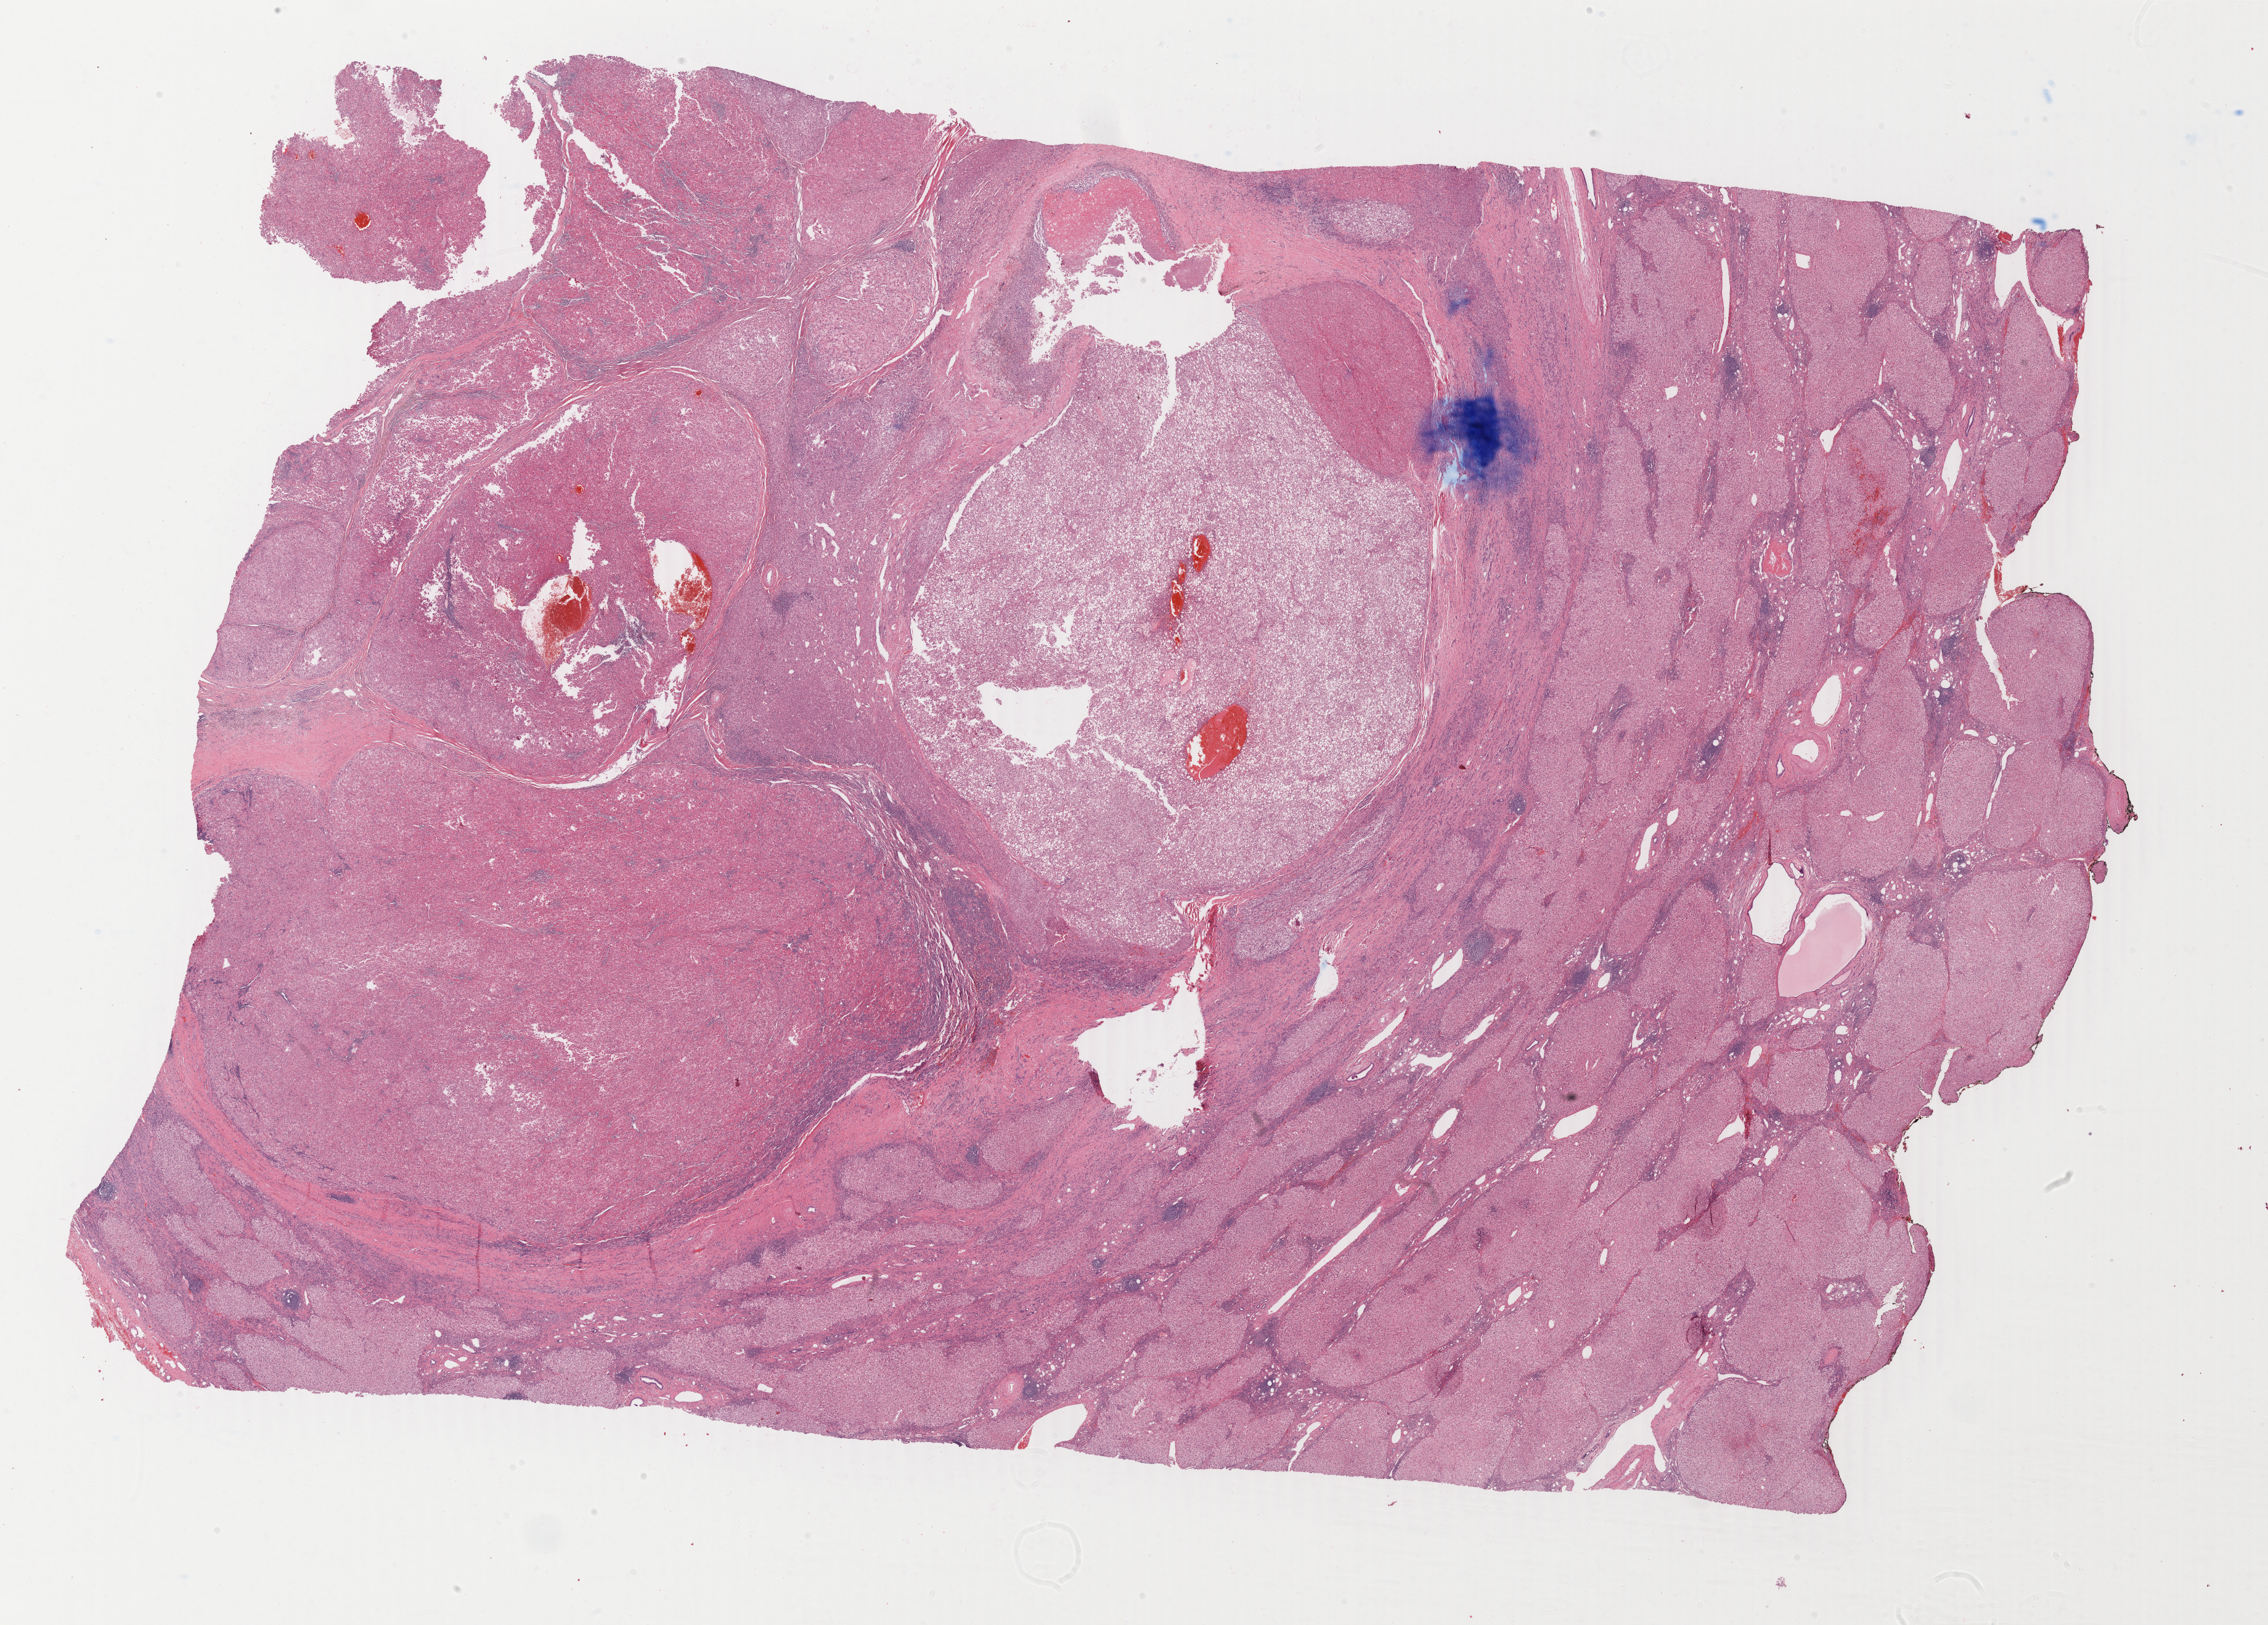
Whole-slide histology image, H&E — a low-resolution overview of the entire scanned area, about 29.3 x 21.0 mm (acquisition: 40x scan), formalin-fixed paraffin-embedded (FFPE) diagnostic section, liver, primary tumour sample. Male patient; age at initial diagnosis 66 years. Histologic grade: G1 (well differentiated).
Pathologic diagnosis: Hepatocellular carcinoma, NOS. AJCC pathologic stage: I (7th edition).